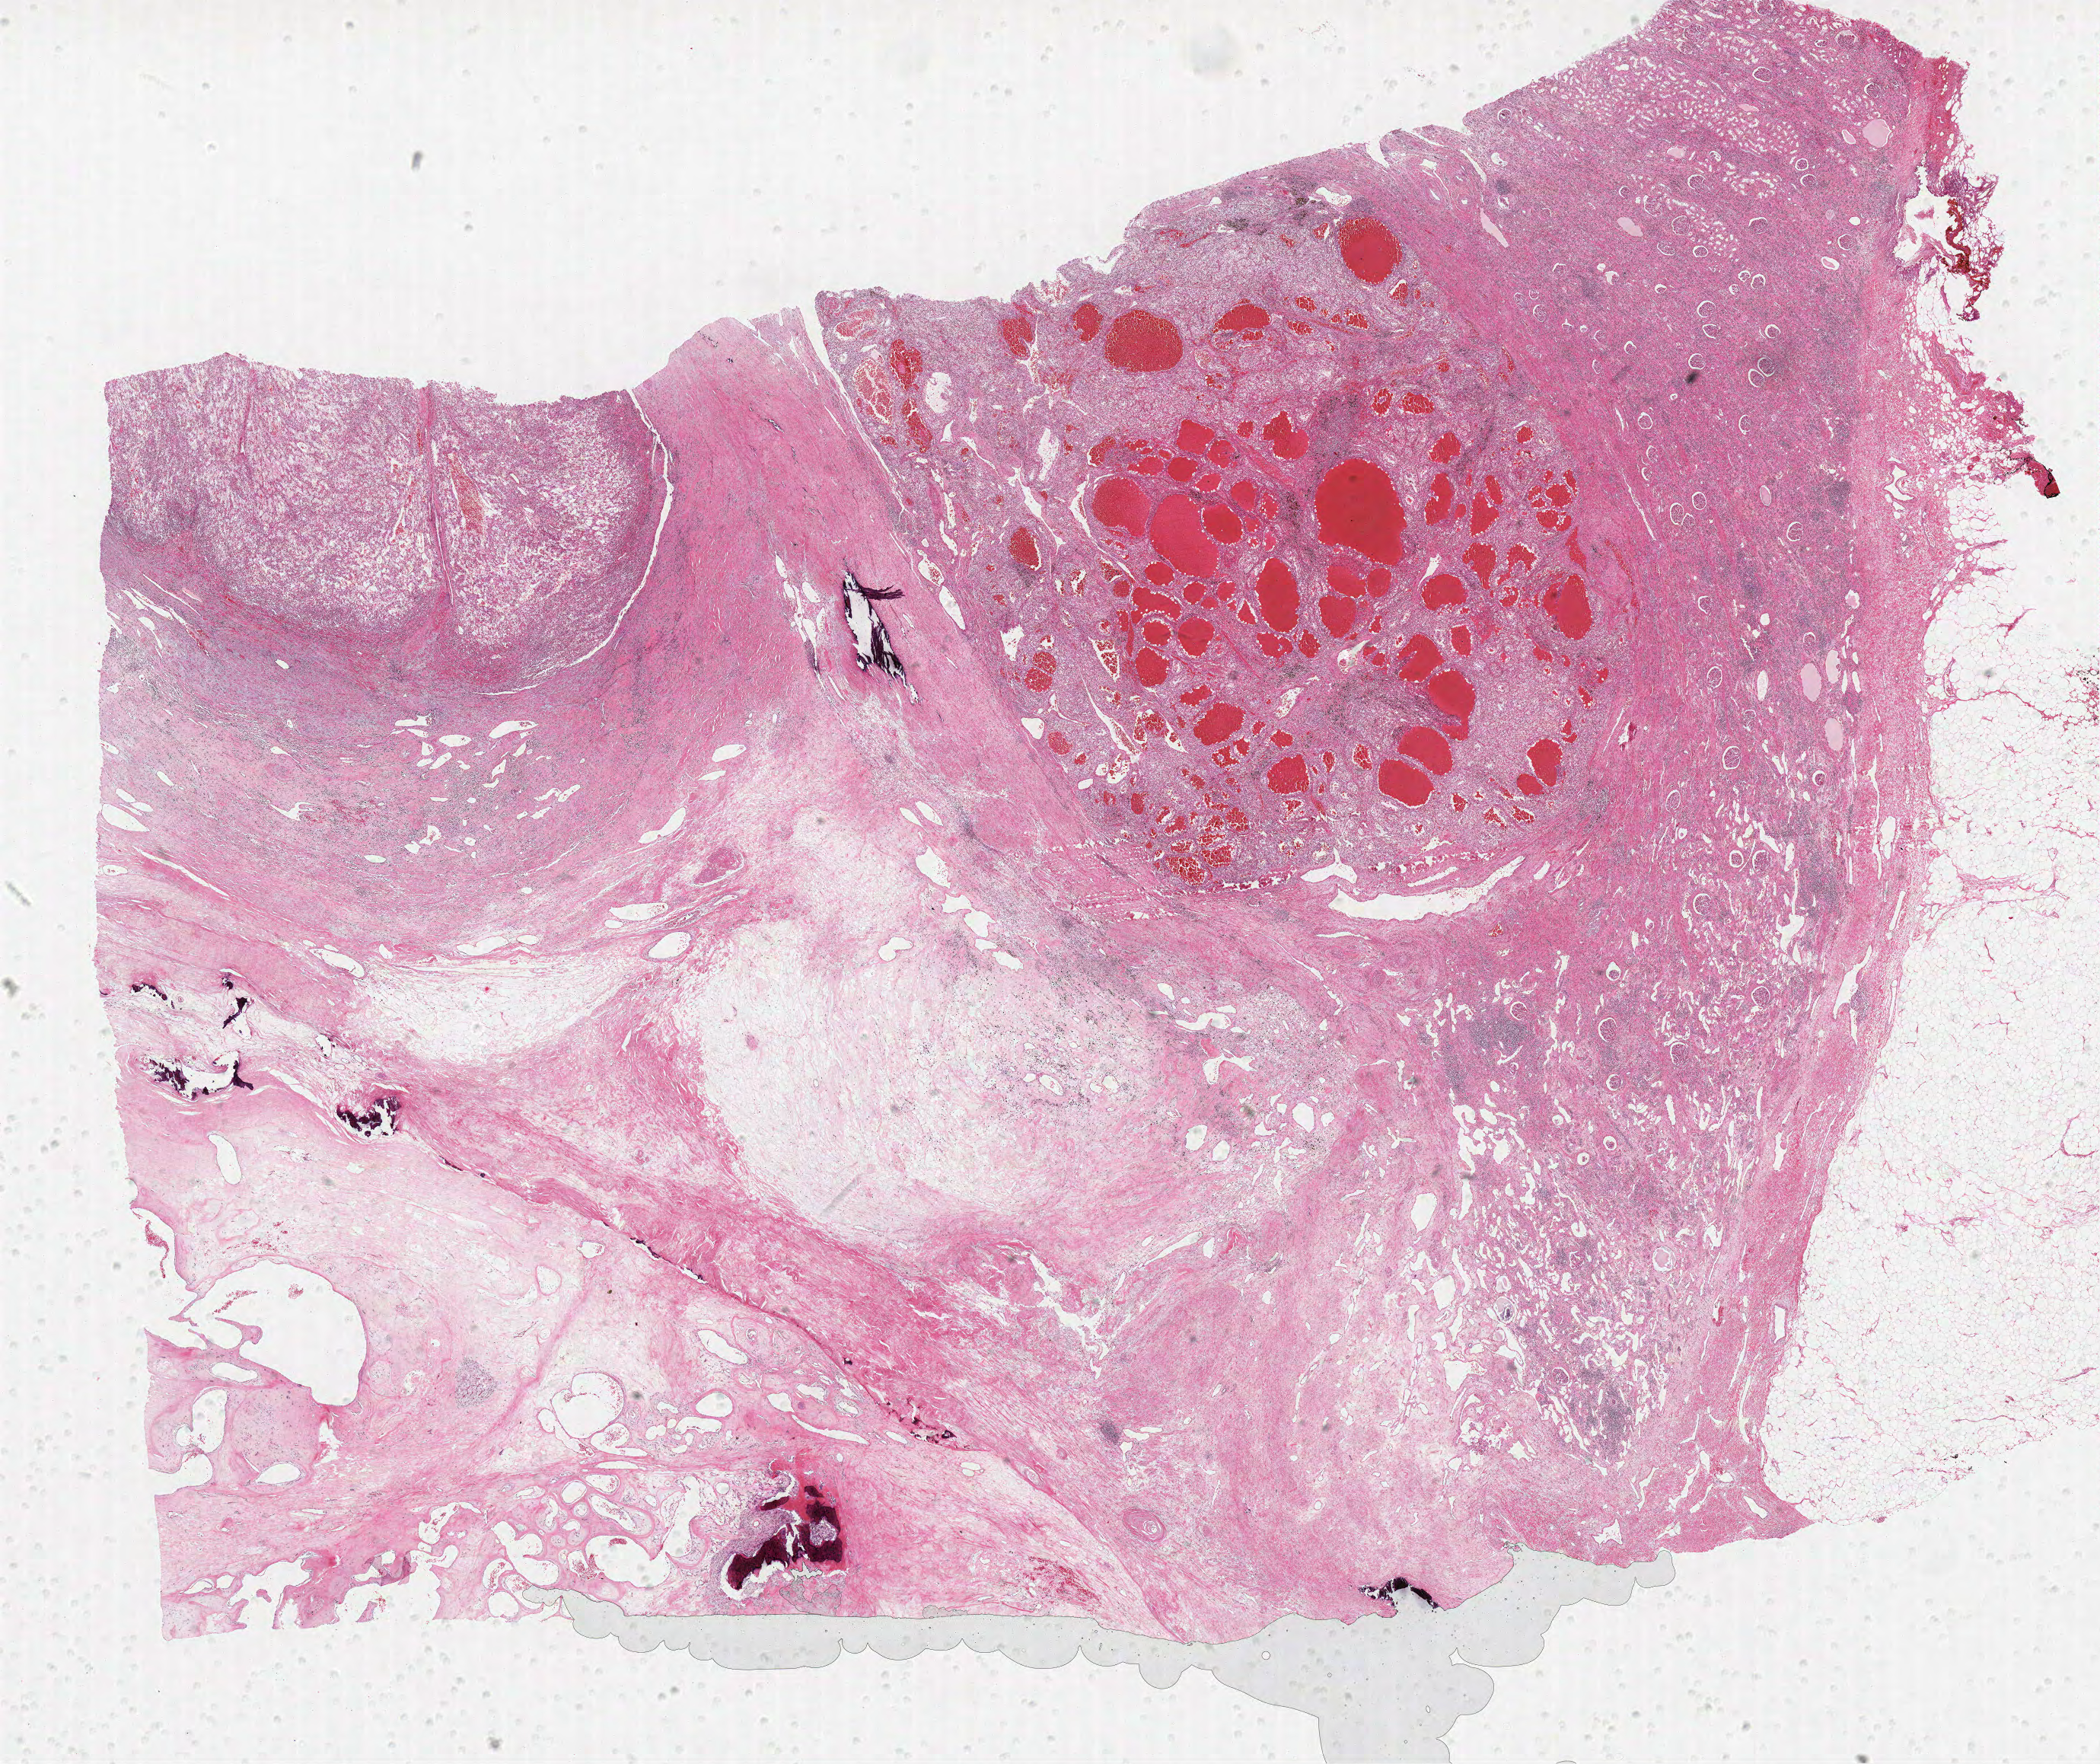
Hematoxylin and eosin (H&E) stained whole-slide image, shown as a low-resolution overview of the whole scanned area (about 22.1 x 18.5 mm), formalin-fixed paraffin-embedded (FFPE) diagnostic section, kidney, primary tumour sample. Male, age 66 years at initial diagnosis. Histologic grade: G4 (undifferentiated).
AJCC pathologic stage: I. Pathologic diagnosis: Clear cell adenocarcinoma, NOS. Laterality: left.